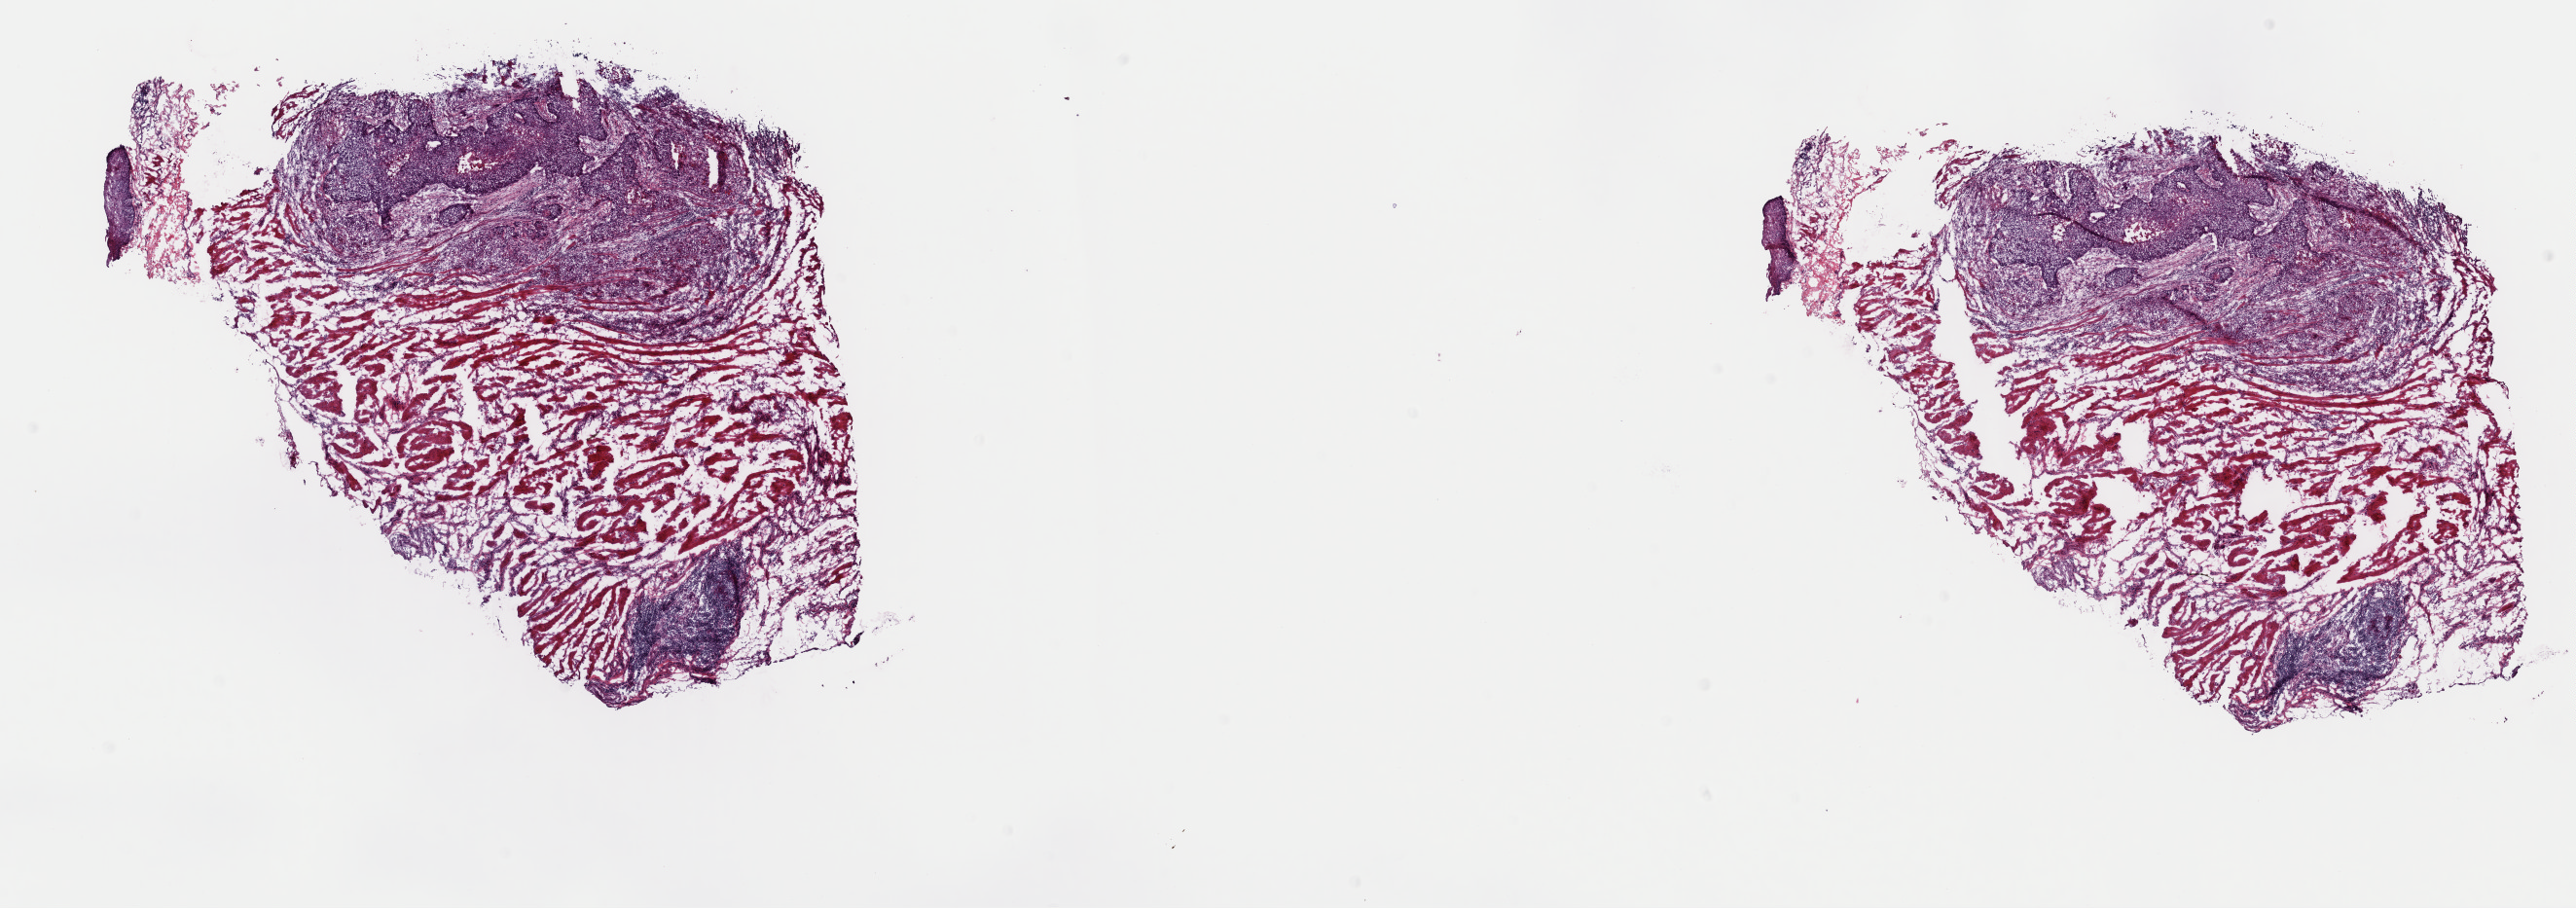
Digitized H&E tissue section (whole slide), low-resolution overview of the scanned area, about 20.9 x 7.4 mm, frozen section from the top of the tissue portion, sample: primary tumour, esophagus. Male, age 53 years at initial diagnosis. Histologic grade: G2 (moderately differentiated). Composition of this section per pathologist review: tumour cells 25%, tumour nuclei 90%, normal cells 30%, stromal cells 44%, necrosis 1%. Inflammatory infiltration, as recorded: lymphocyte infiltration 10%, monocyte infiltration 1%, neutrophil infiltration 1%.
AJCC pathologic stage: IIIA (7th edition). TNM: T4 N0 M0. Diagnosis: Squamous cell carcinoma, NOS (lower third of esophagus).